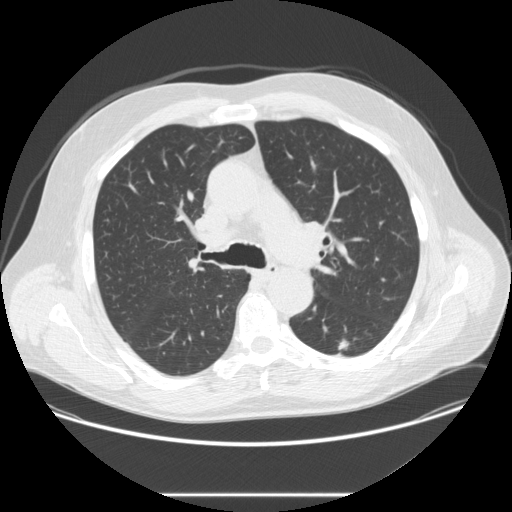
Low-dose screening chest CT, one axial slice; slice 168 of 262 in the series (ordered by position); reconstruction kernel STANDARD; 120 kVp; lung window (W 1500 / L -600 HU); 512 × 512 image matrix, field of view 420 × 420 mm.
Structures marked on this image (outlined manually by an expert reader):
- lesion 1 (tumor, lower lobe of left lung): box from (x=338, y=339) to (x=349, y=350) px